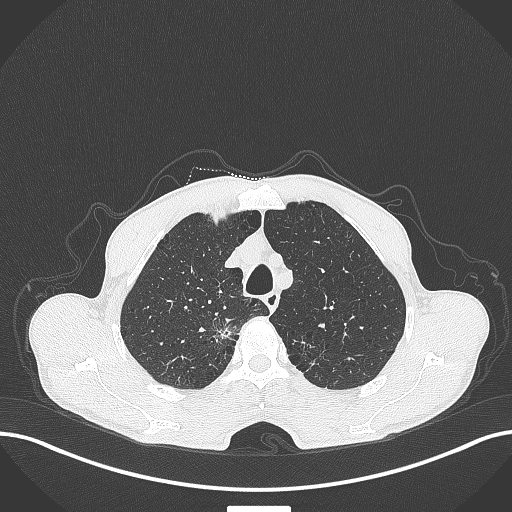
Chest CT, one axial slice; position 345 of 445 along the scan axis; reconstruction kernel B70f; 120 kVp; lung window (W 1500 / L -600 HU); 512 × 512 image matrix, field of view 400 × 400 mm. Patient: male, 70 years. Case-level facts recorded for this patient, not image findings: clinical TNM (as recorded): T1a N0 M0; histopathological grade: G1-2.
Annotated regions visible in this slice (rectangle marked by the reading radiologist):
- lung tumour (recorded histology: adenocarcinoma): box from (x=213, y=320) to (x=237, y=343) px